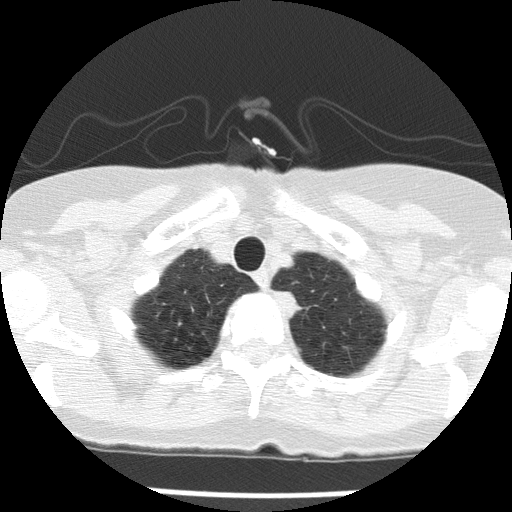
Low-dose screening chest CT, one axial slice. Position 129 of 143 along the scan axis. Reconstruction kernel FC51. 120 kVp. Lung window (W 1500 / L -600 HU). 2 mm slice thickness. 512 × 512 image matrix.
Annotated regions visible in this slice (expert manual segmentation):
- lesion 1 (tumor, upper lobe of left lung): box from (x=273, y=291) to (x=303, y=319) px